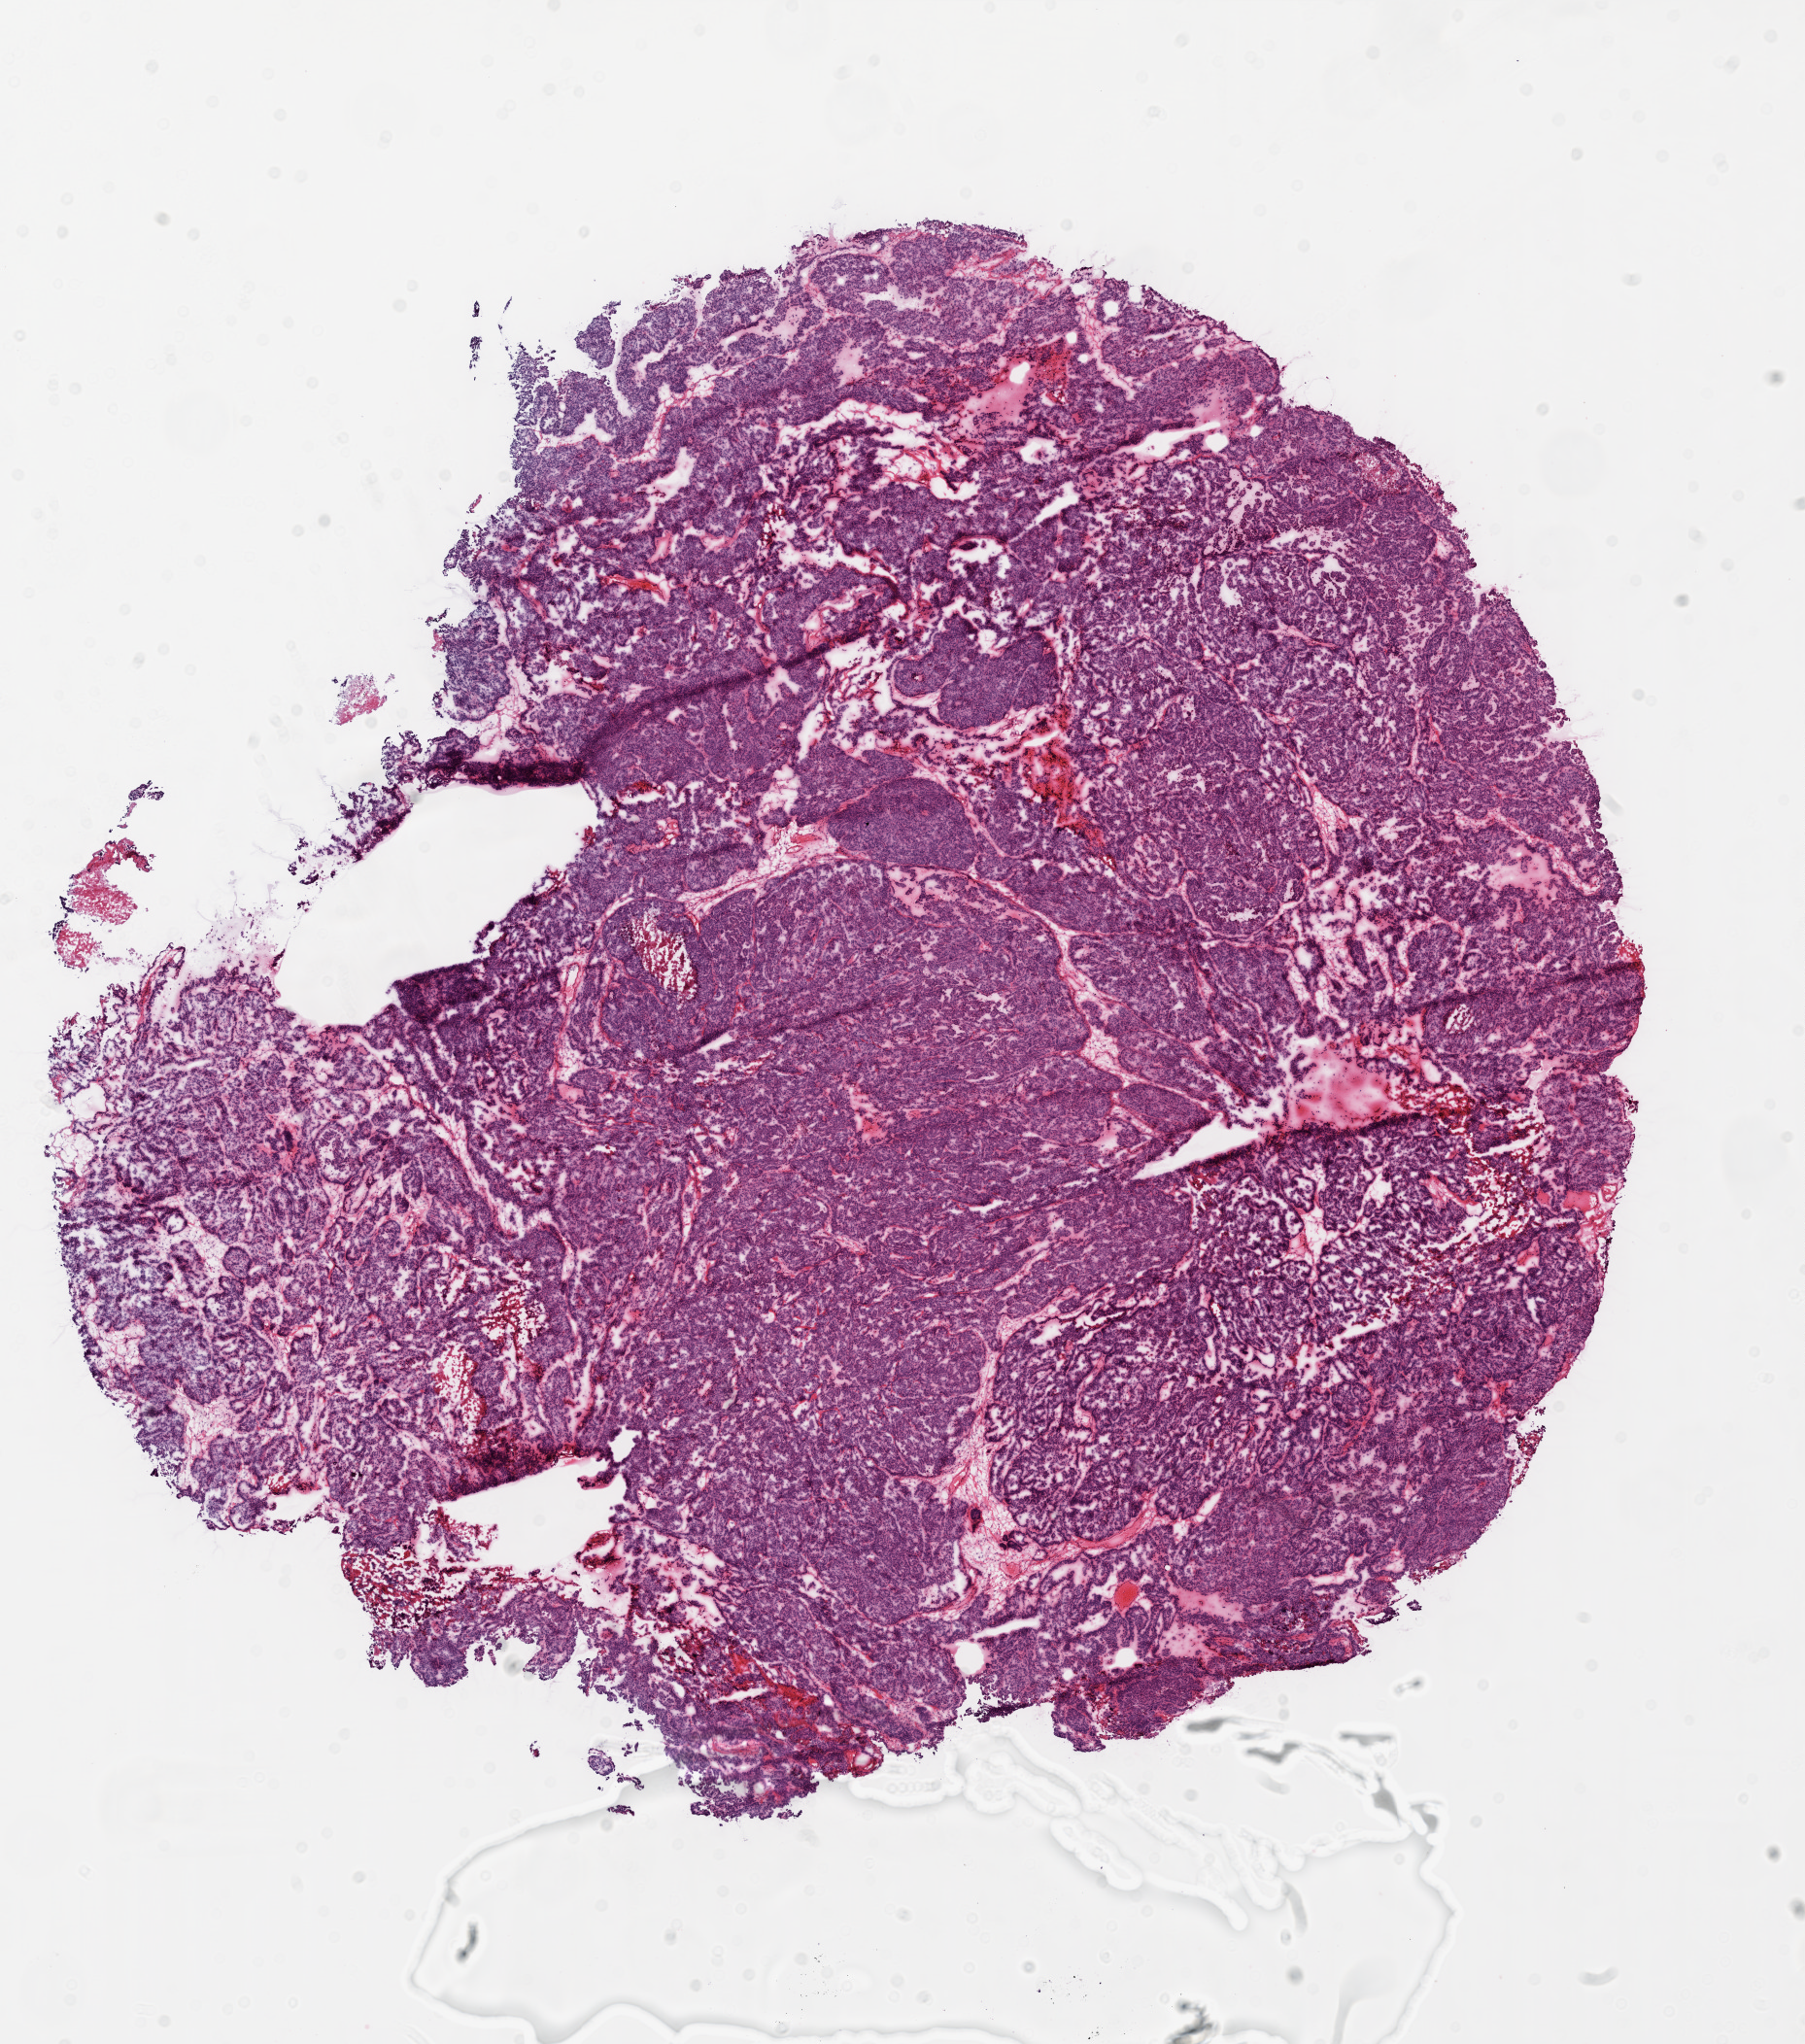
H&E-stained whole-slide image — whole scanned area (about 14.9 x 16.9 mm) shown as a low-resolution overview. Frozen section from the top of the tissue portion. Ovary, primary tumour sample. Patient: female, age at initial diagnosis 60 years. Histologic grade: G3 (poorly differentiated). Composition of this section per pathologist review: tumour cells 95%, tumour nuclei 98%, normal cells 0%, stromal cells 5%, necrosis 0%.
* laterality: bilateral
* FIGO stage: IIIC
* diagnosis: Serous cystadenocarcinoma, NOS